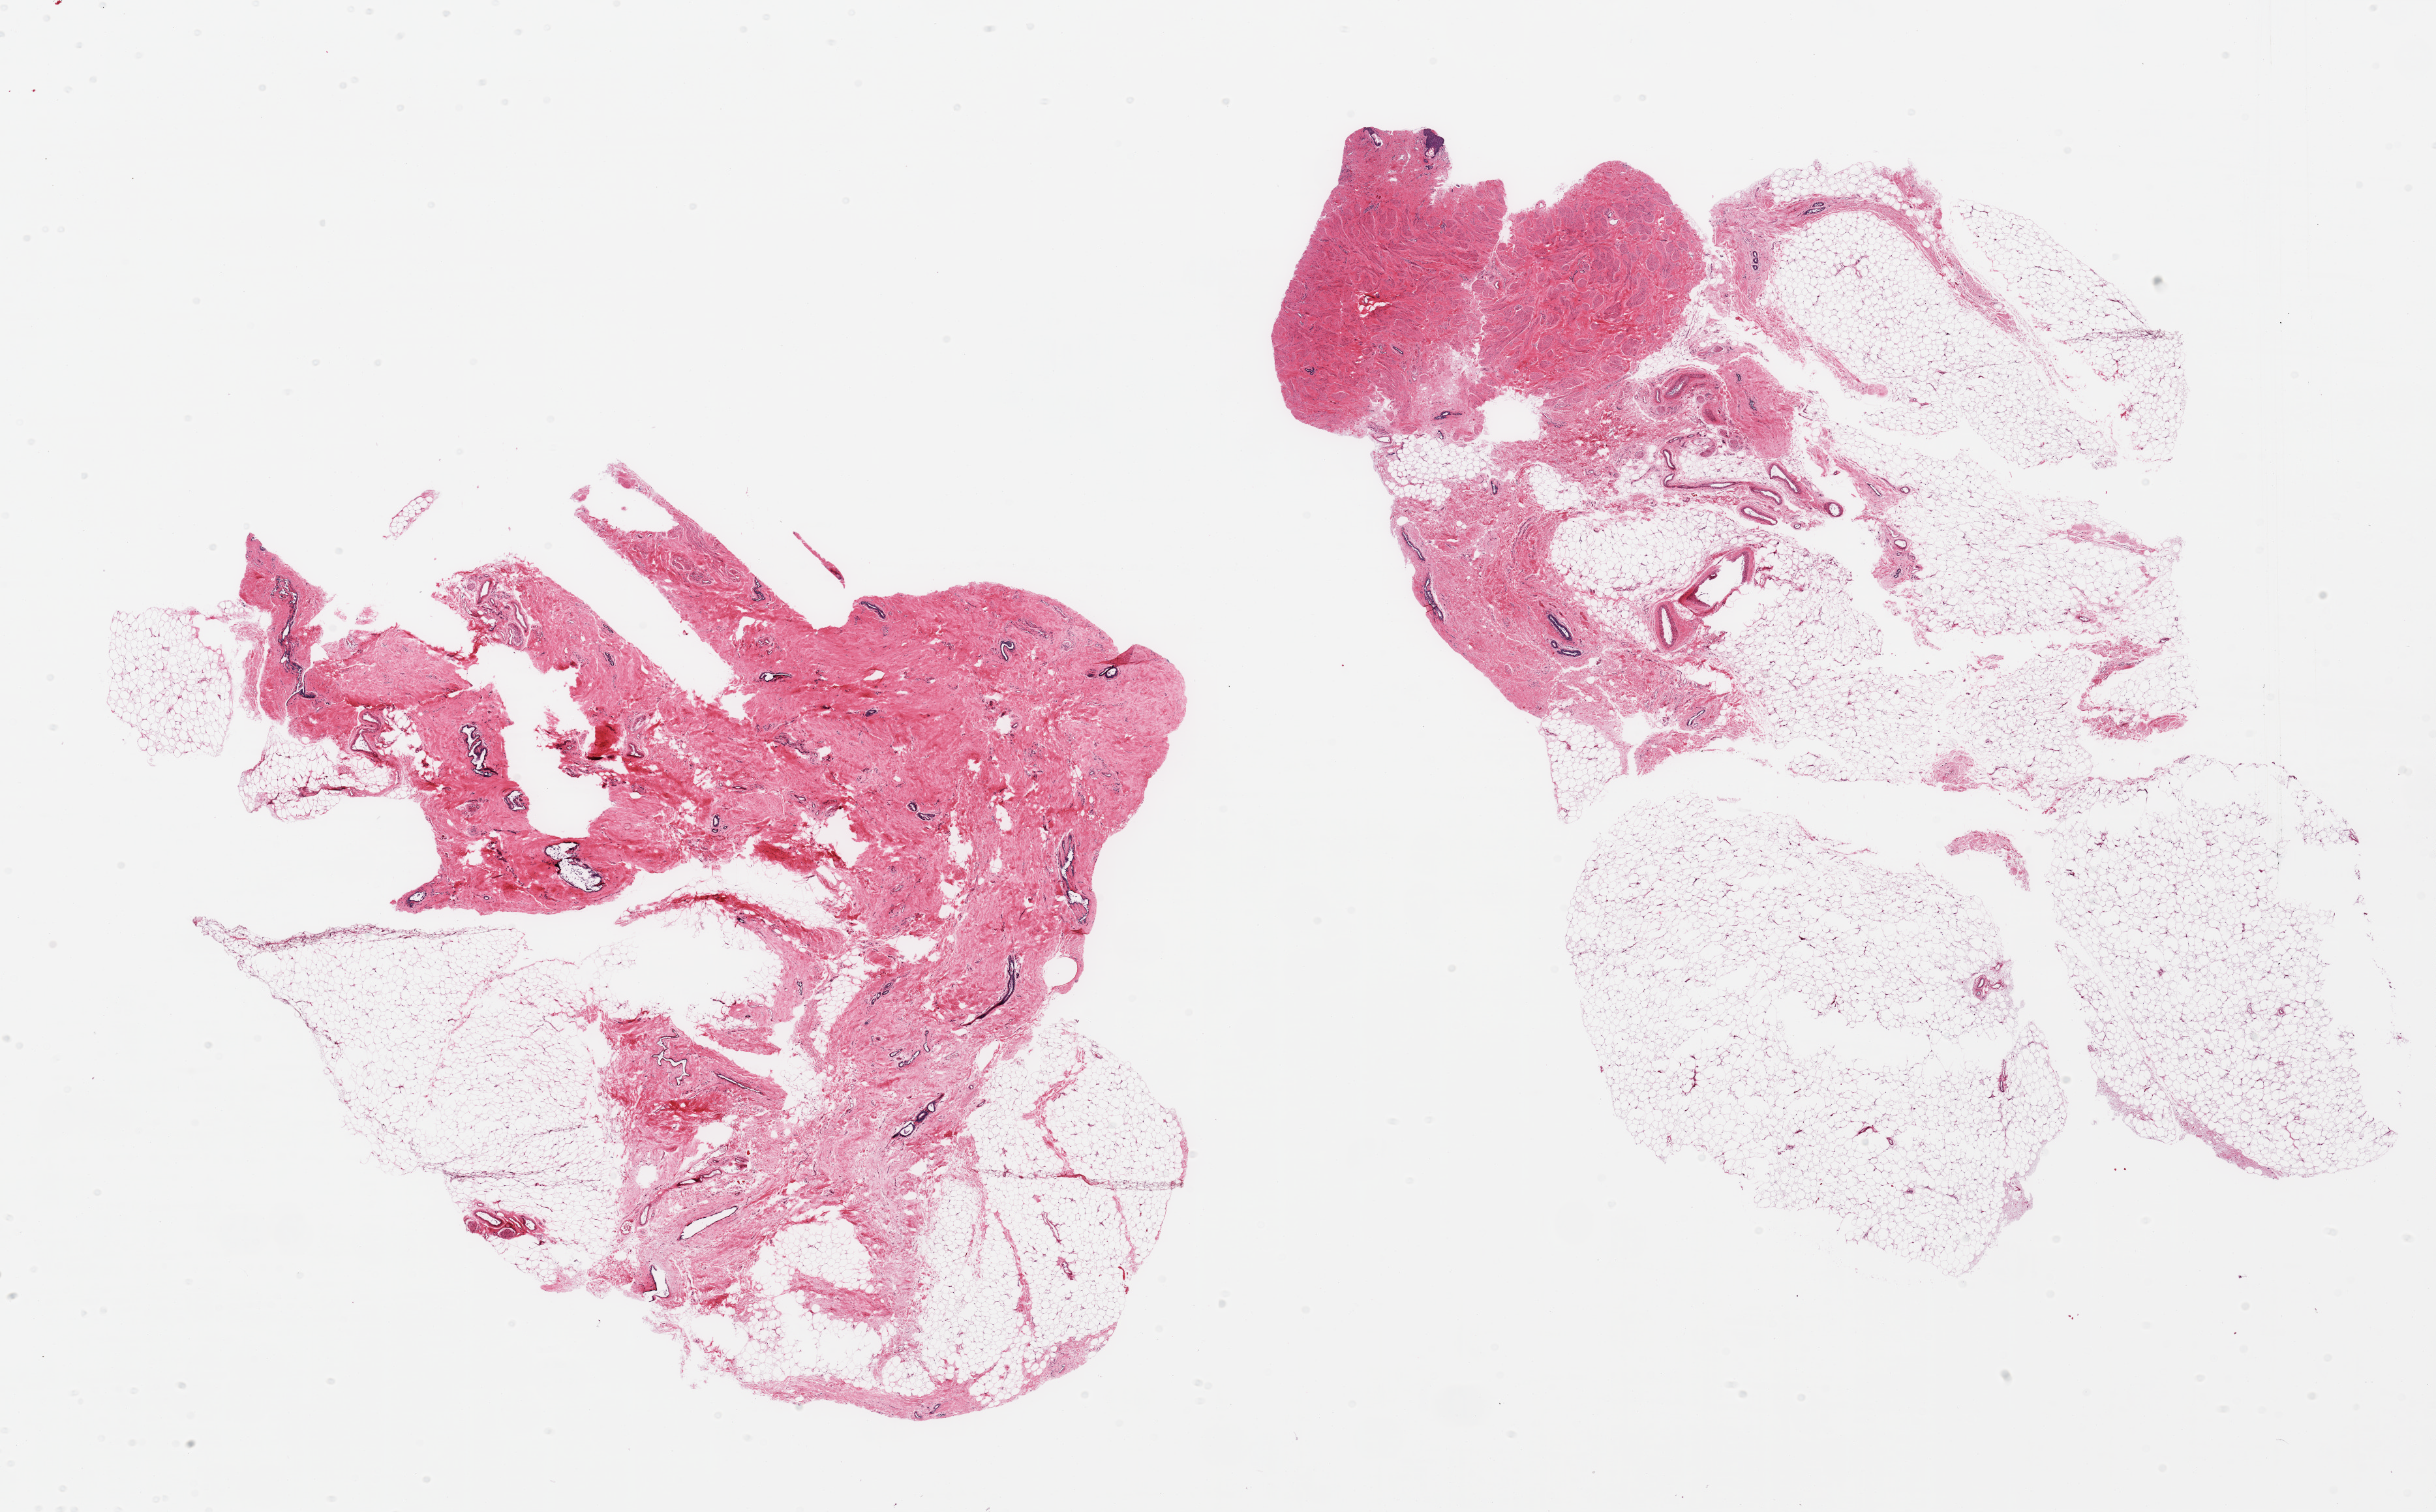
Whole-slide image, haematoxylin and eosin stain — shown as a low-resolution overview of the whole scanned area (about 29.5 x 18.3 mm), PAXgene-fixed paraffin-embedded (PFPE) section, section of breast (target tissue), donor tissue sample.
Pathologist's review note for this sample: 2 pieces, gynecomastoid stromal and dcutal hyperplasia.